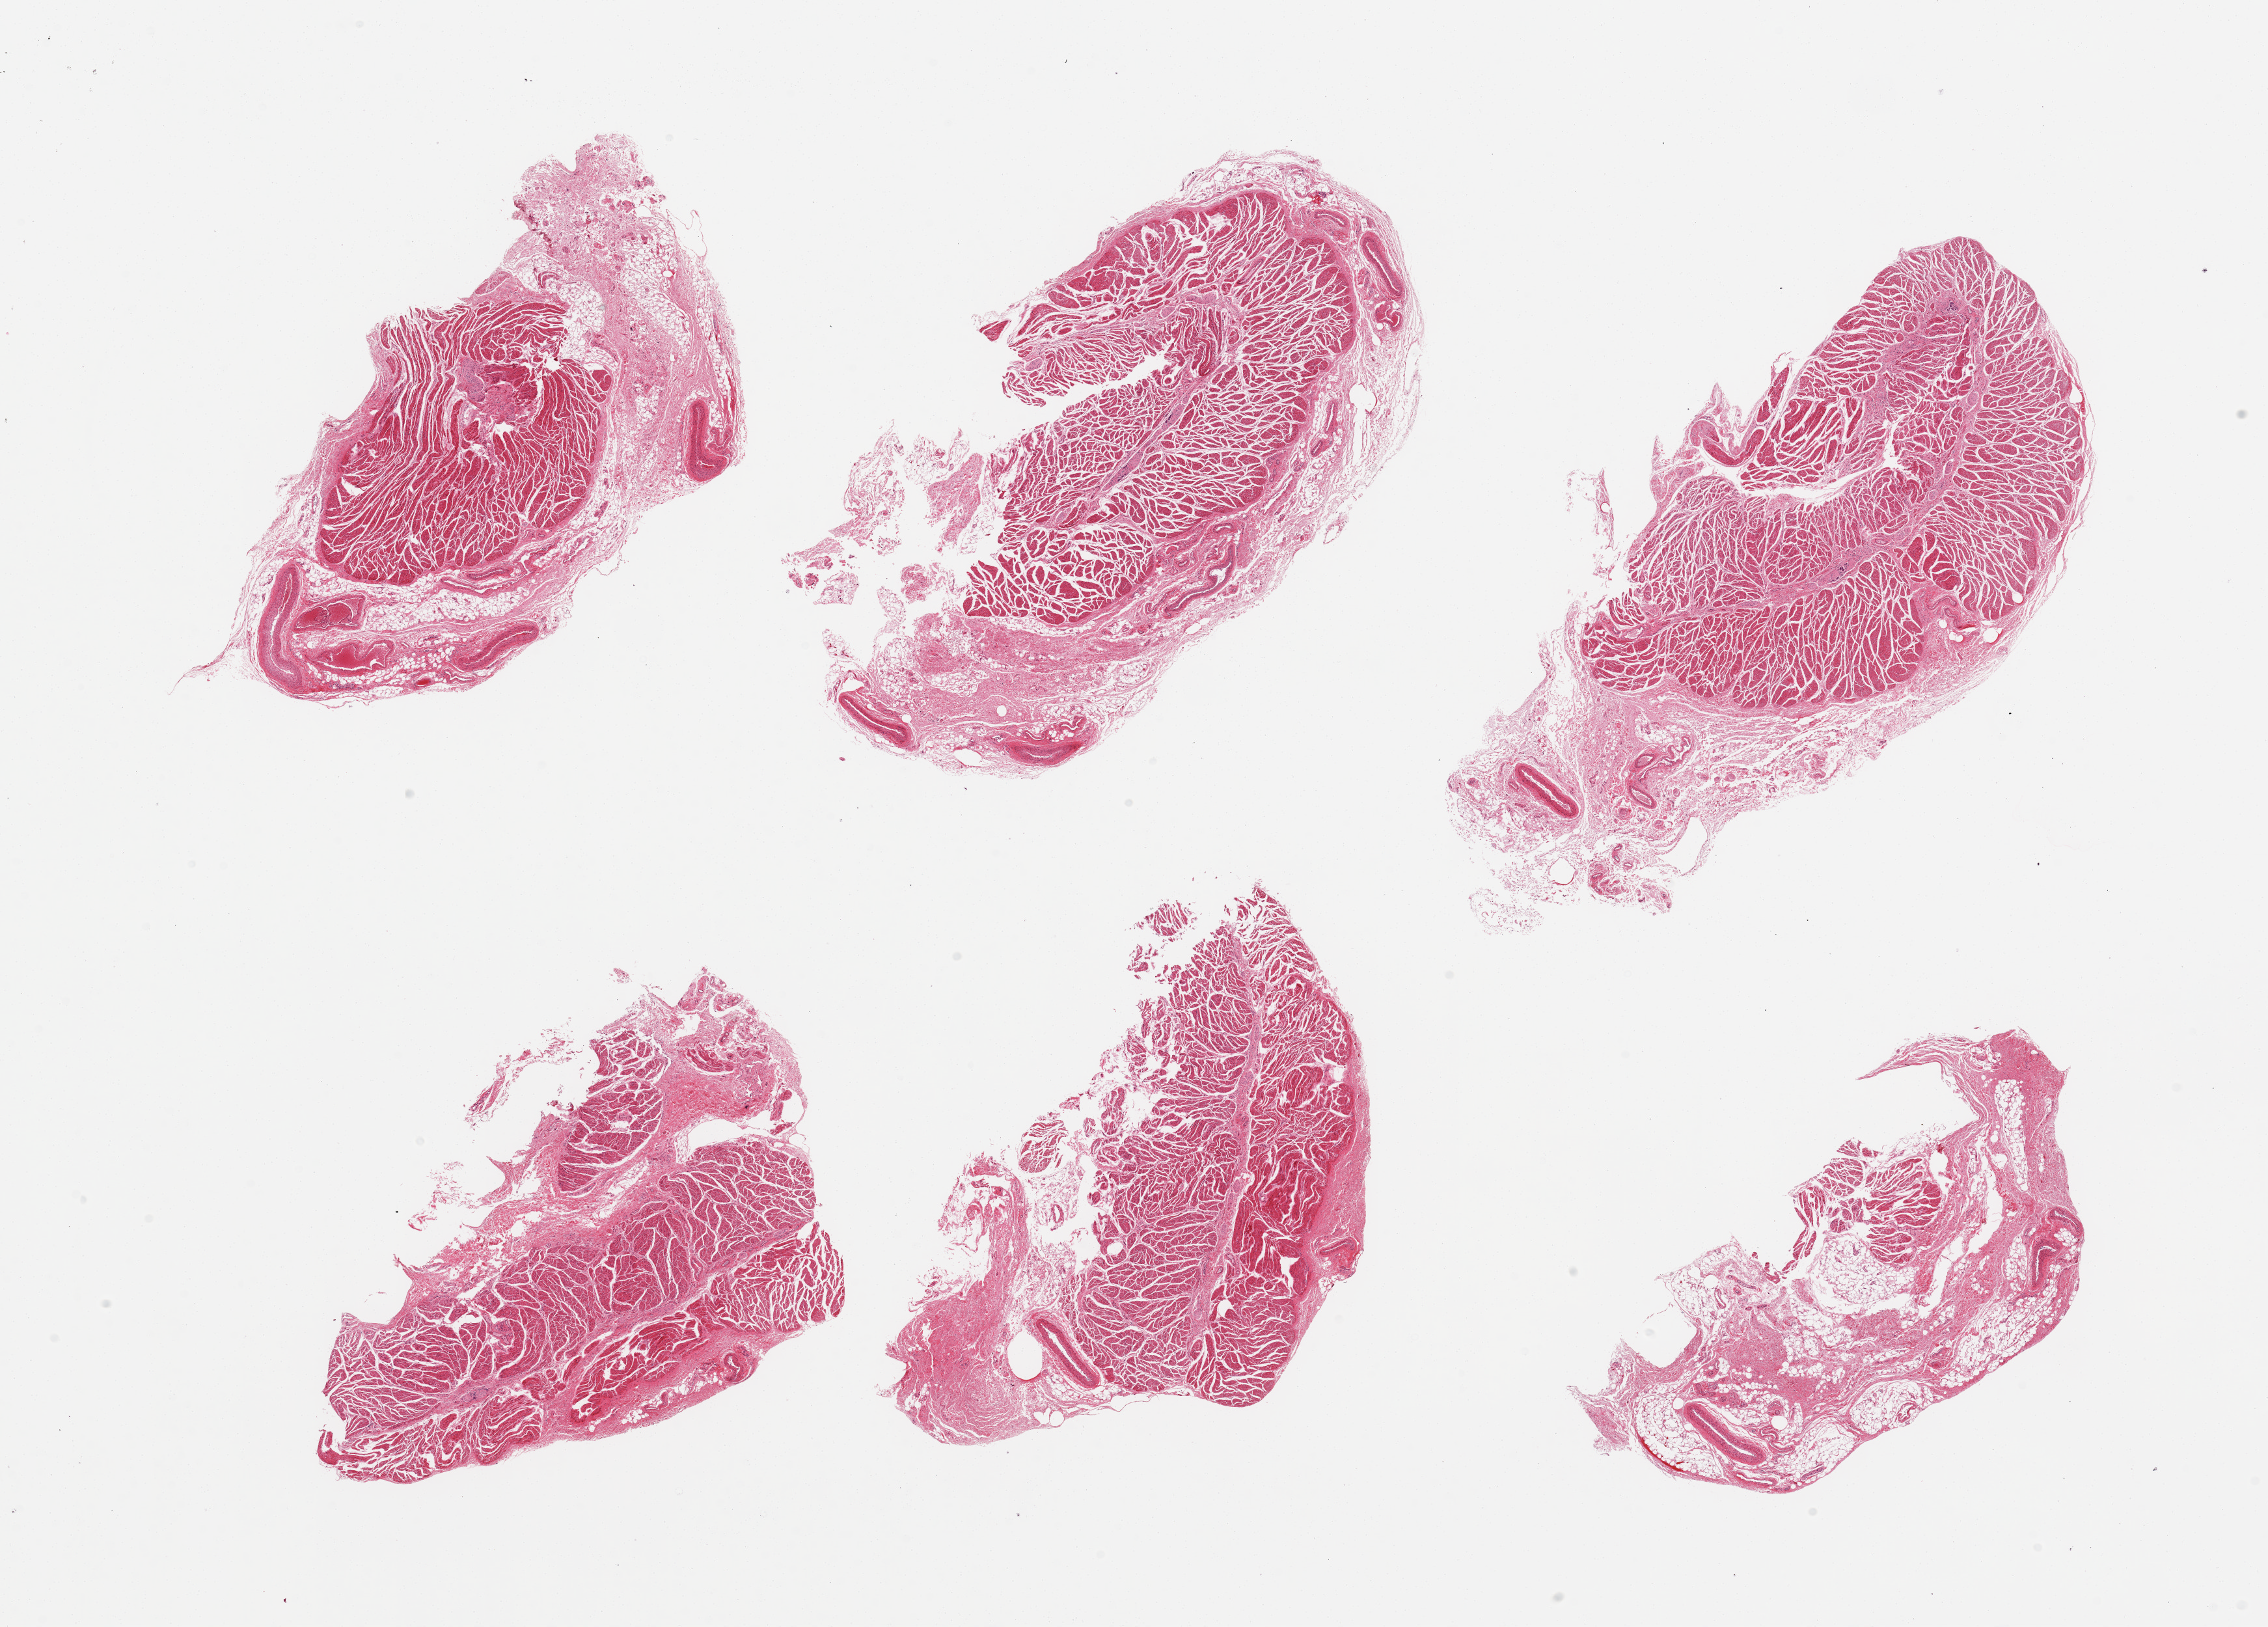
Haematoxylin and eosin whole-slide image, a low-resolution overview of the entire scanned area, about 27.6 x 19.8 mm (acquisition: 20x scan). PAXgene-fixed, paraffin-embedded tissue. Target tissue: gastroesophageal junction. Tissue donor sample. Donor: male.
- pathologist's review note for this sample: 6 pieces, few foci of admixed fat